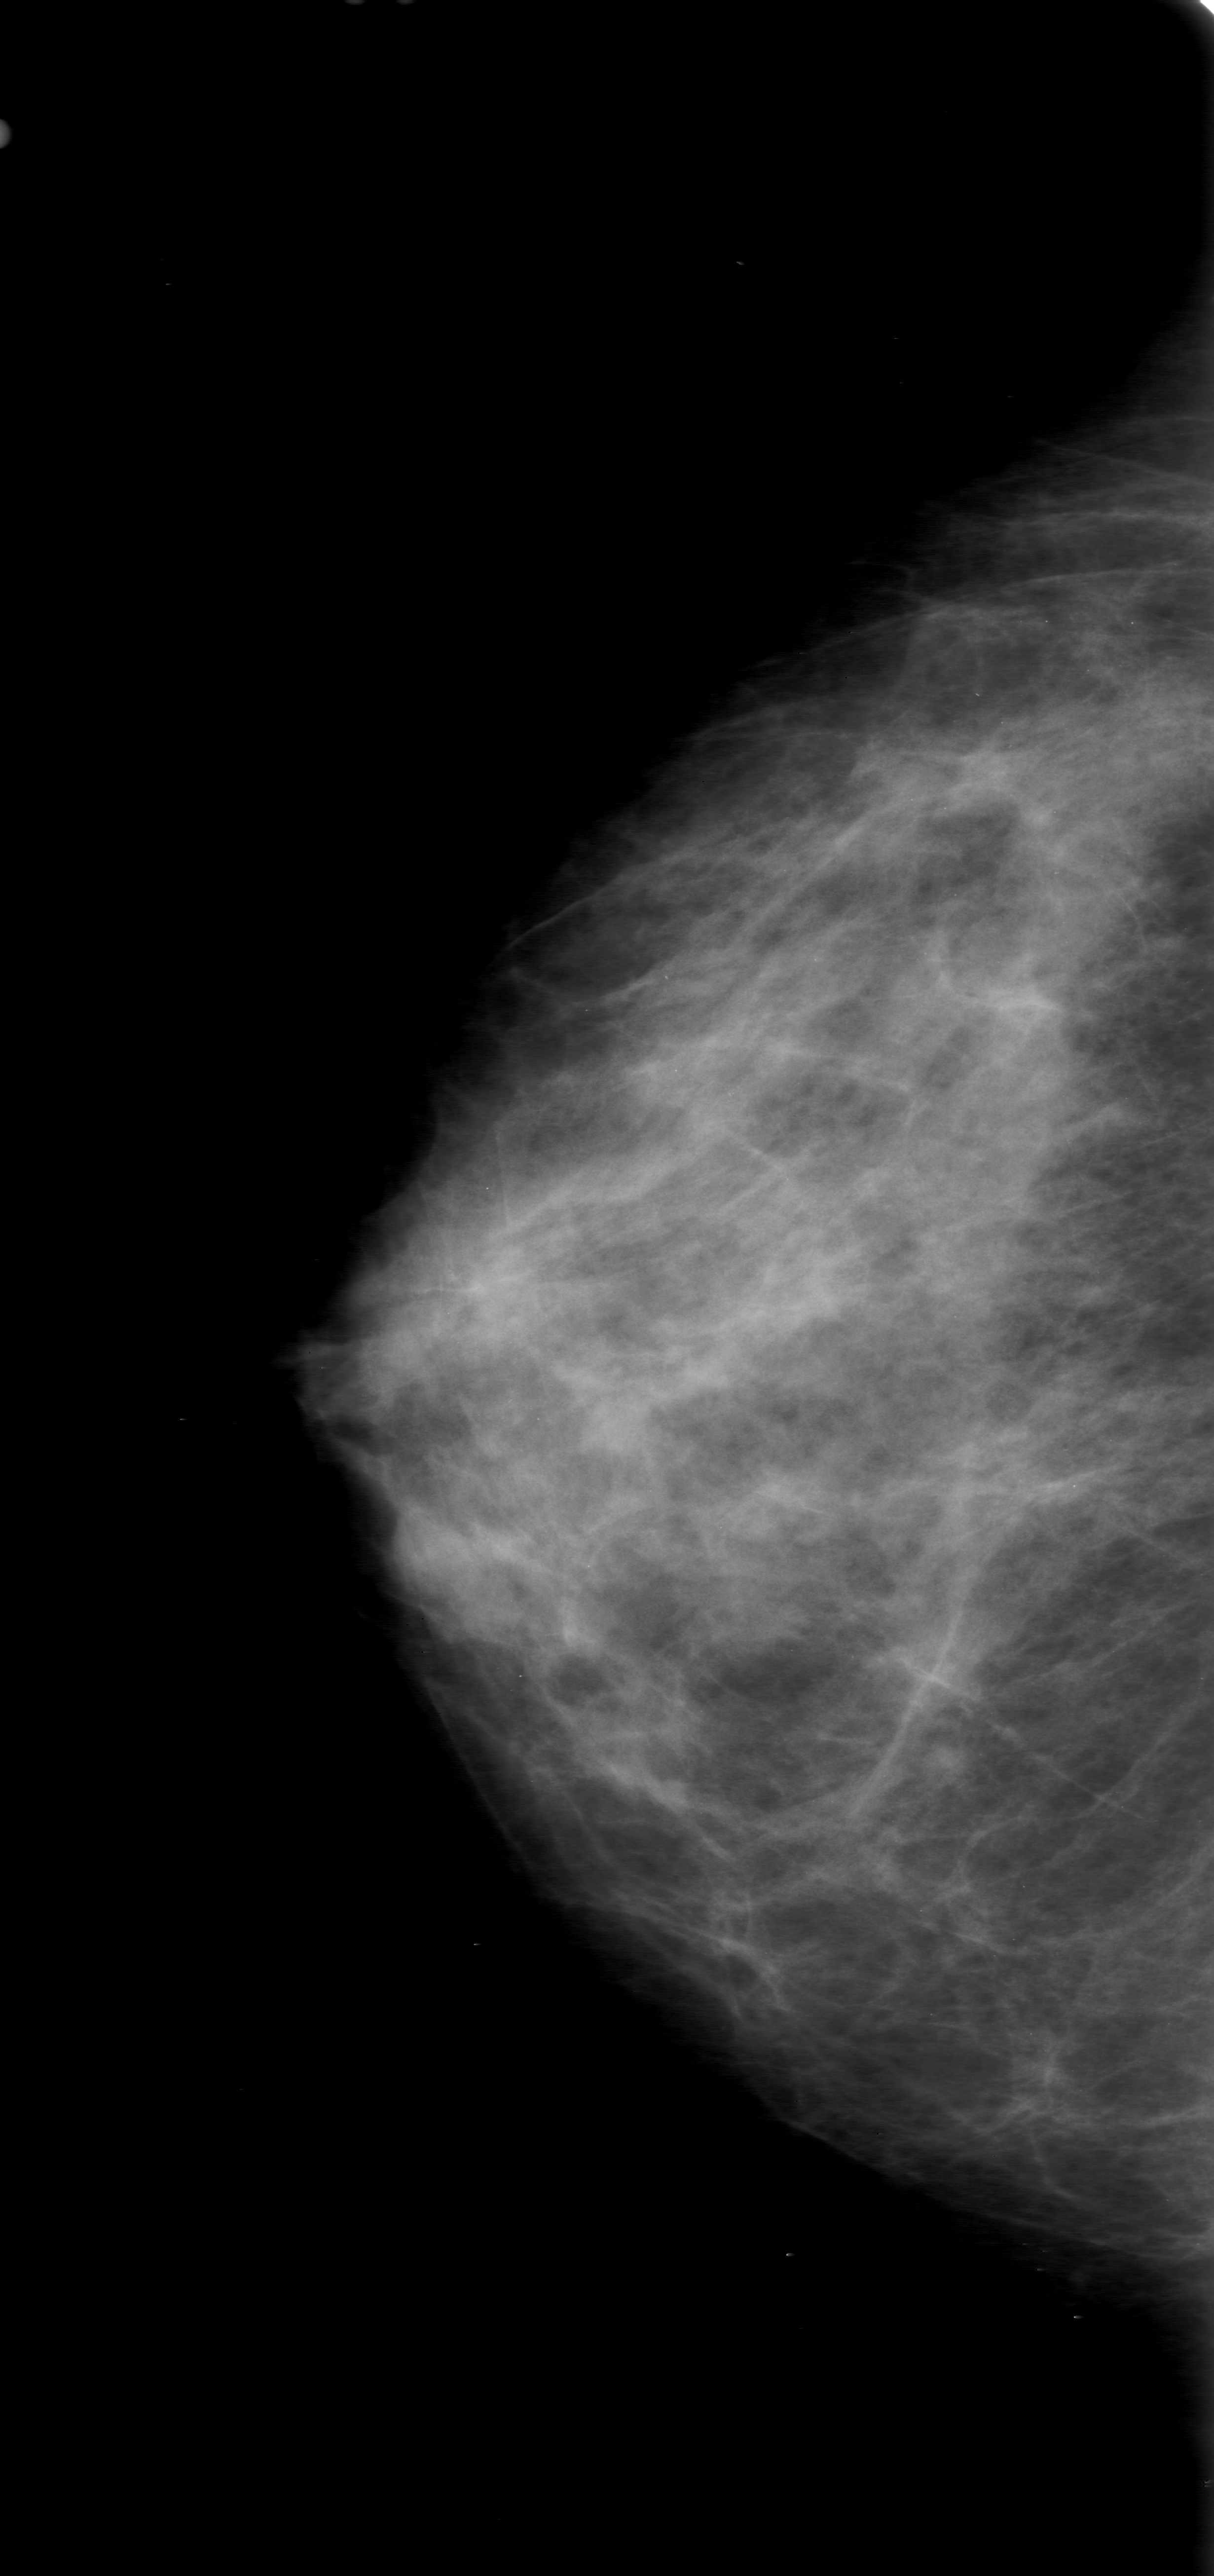
Mammogram (digitized film); right breast; CC view.
Finding: mass, shape oval, margins obscured; BI-RADS assessment category 0 (incomplete: needs additional imaging); subtlety rating 4 on a 1 (subtle) to 5 (obvious) scale; pathology (as recorded): benign.